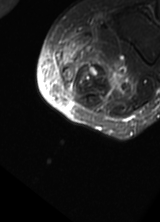
MRI of an extremity soft-tissue mass, one axial slice; position 4 of 69 along the scan axis; T2-weighted fat-saturated; MR volume resampled by the dataset authors to the PET/CT grid (not the native acquisition matrix); 3.27 mm slice thickness; 160 × 222 image matrix, field of view 156 × 217 mm. Female patient. Case-level facts recorded for this patient, not image findings: histological type: pleomorphic leiomyosarcoma; grade: high; site of the primary tumour: left thigh.
Annotated regions visible in this slice (expert contour drawn on MRI and transferred to this co-registered scan by the dataset authors):
- gross tumour volume including surrounding oedema: bounding box <59,29,135,105> (left, top, right, bottom; pixels)